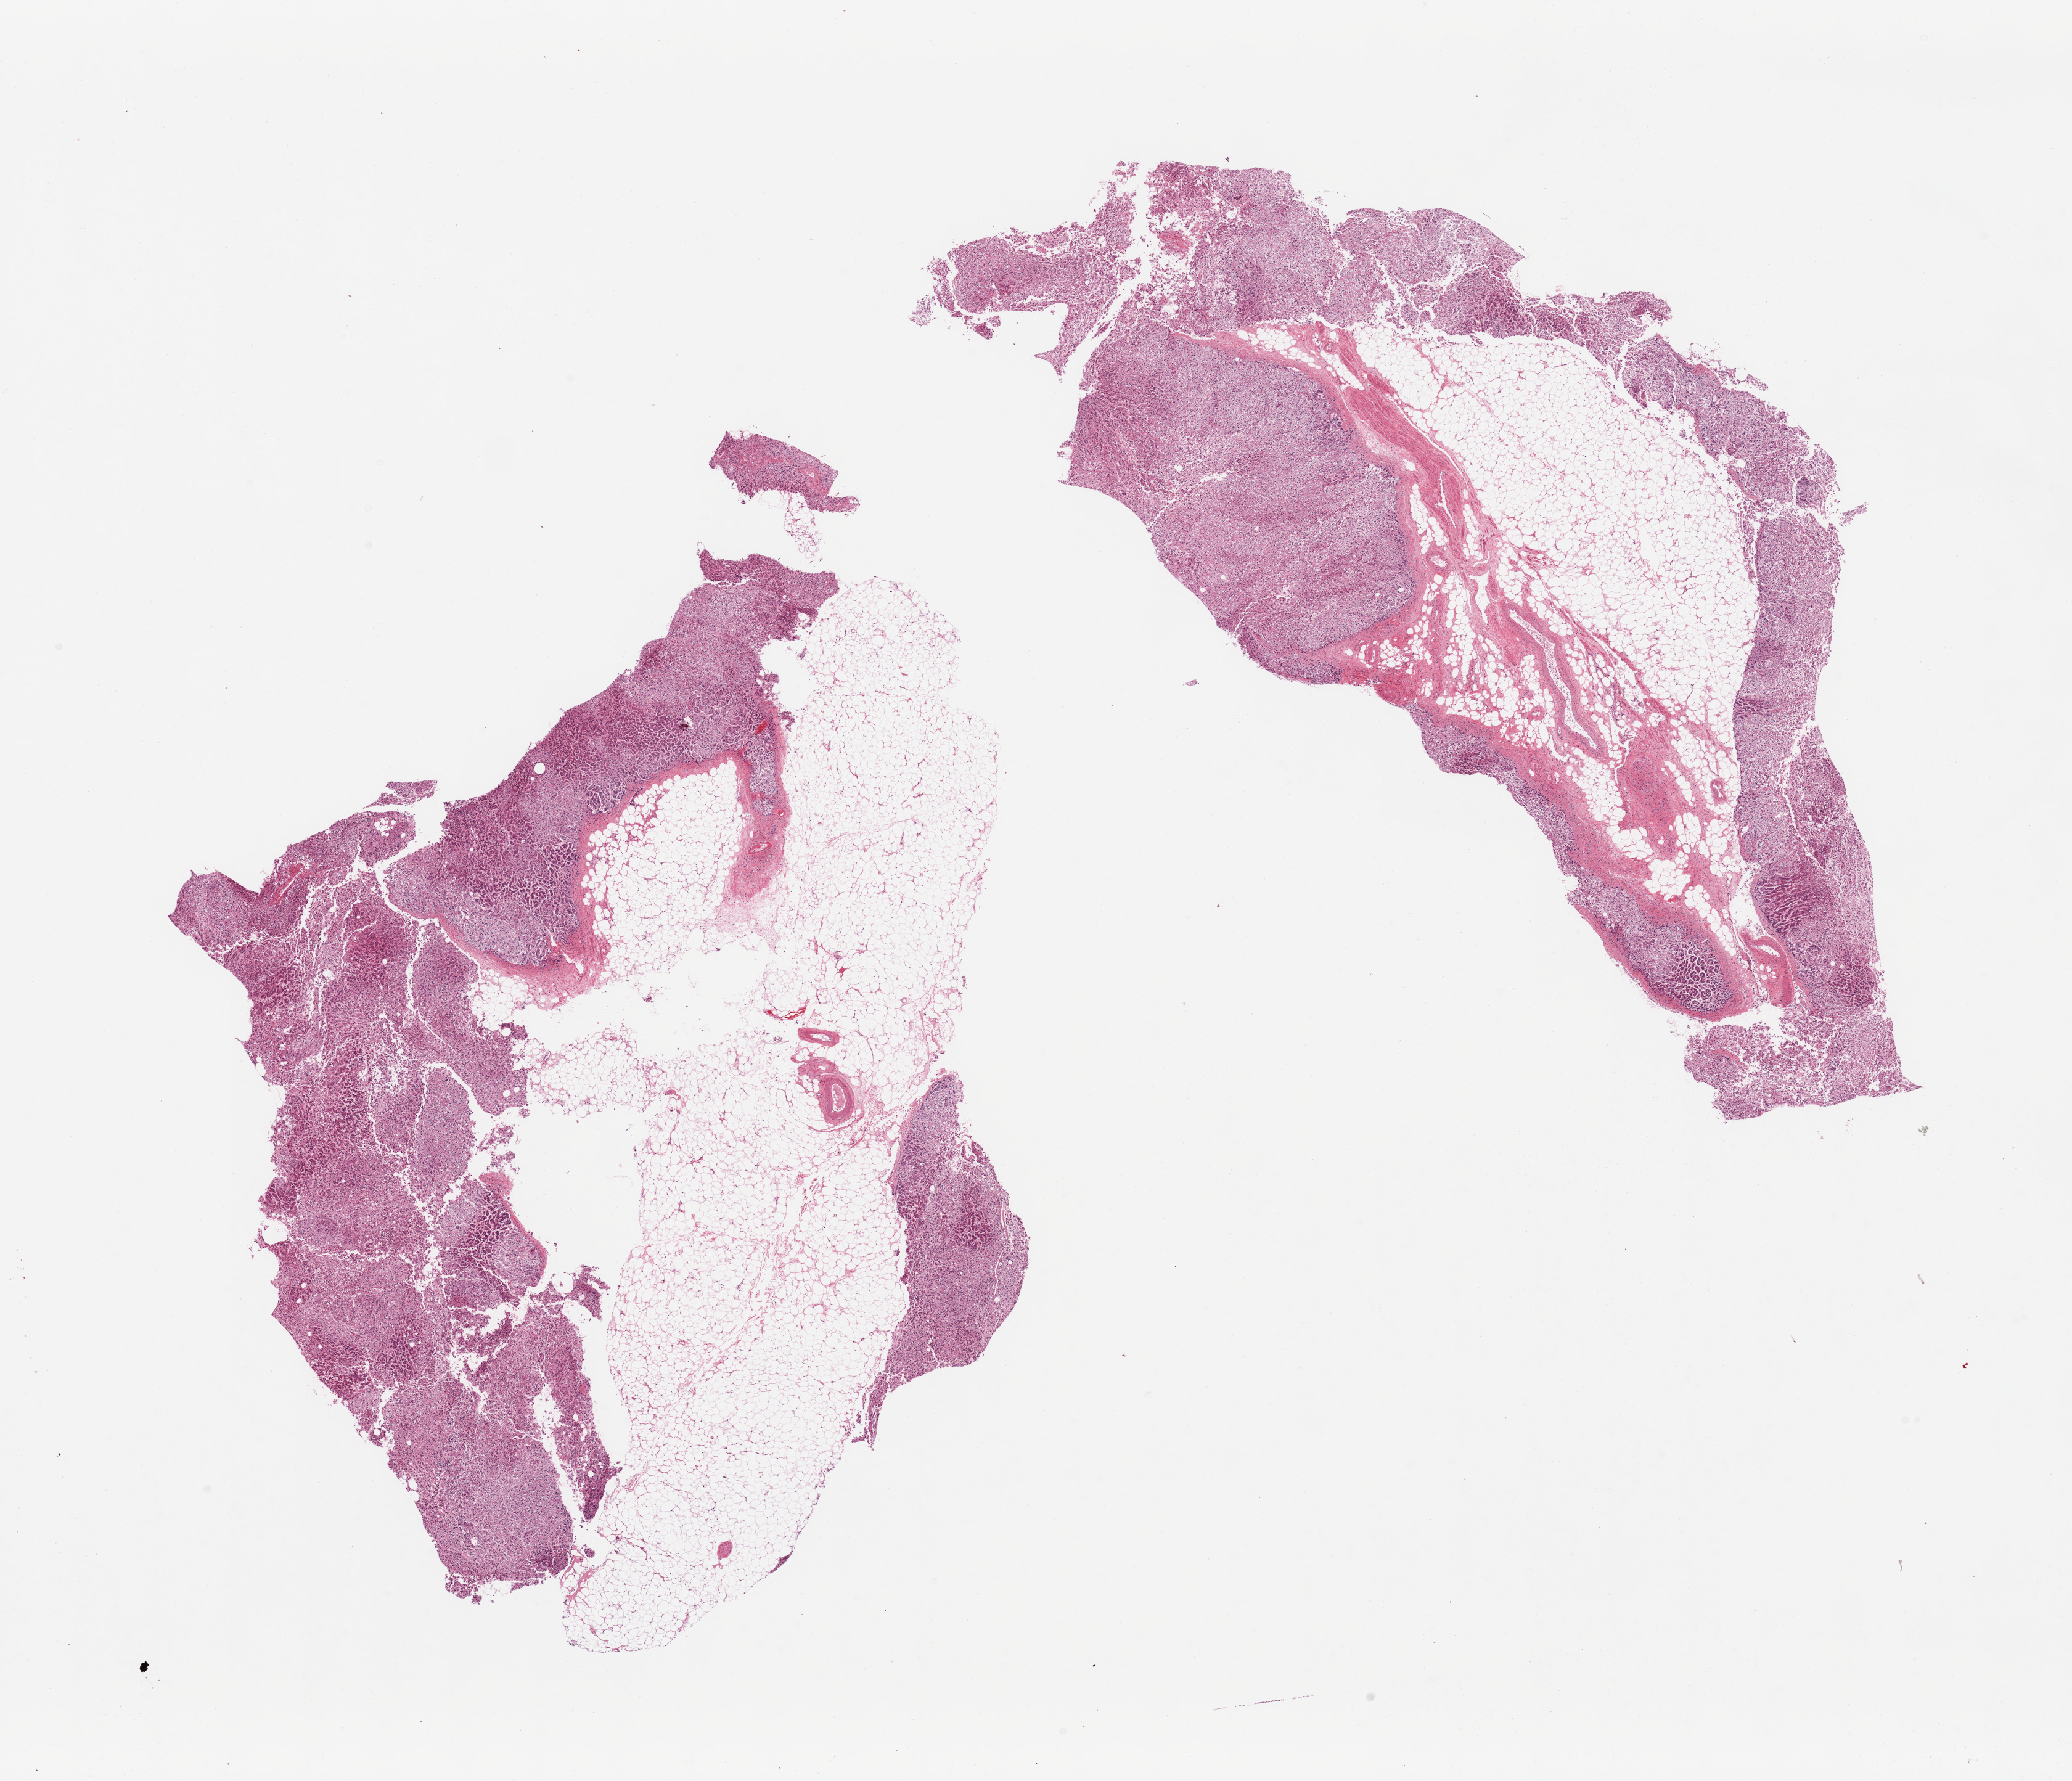
Digitized H&E-stained section, low-resolution overview of the scanned area, about 26.6 x 22.8 mm (acquisition: 20x scan). PAXgene-fixed paraffin-embedded (PFPE) section. Section of adrenal gland (target tissue). Tissue donor sample. Donor: male.
* reviewer comment on this tissue sample: 2 pieces, both ~50% fat with large vessel and nerve